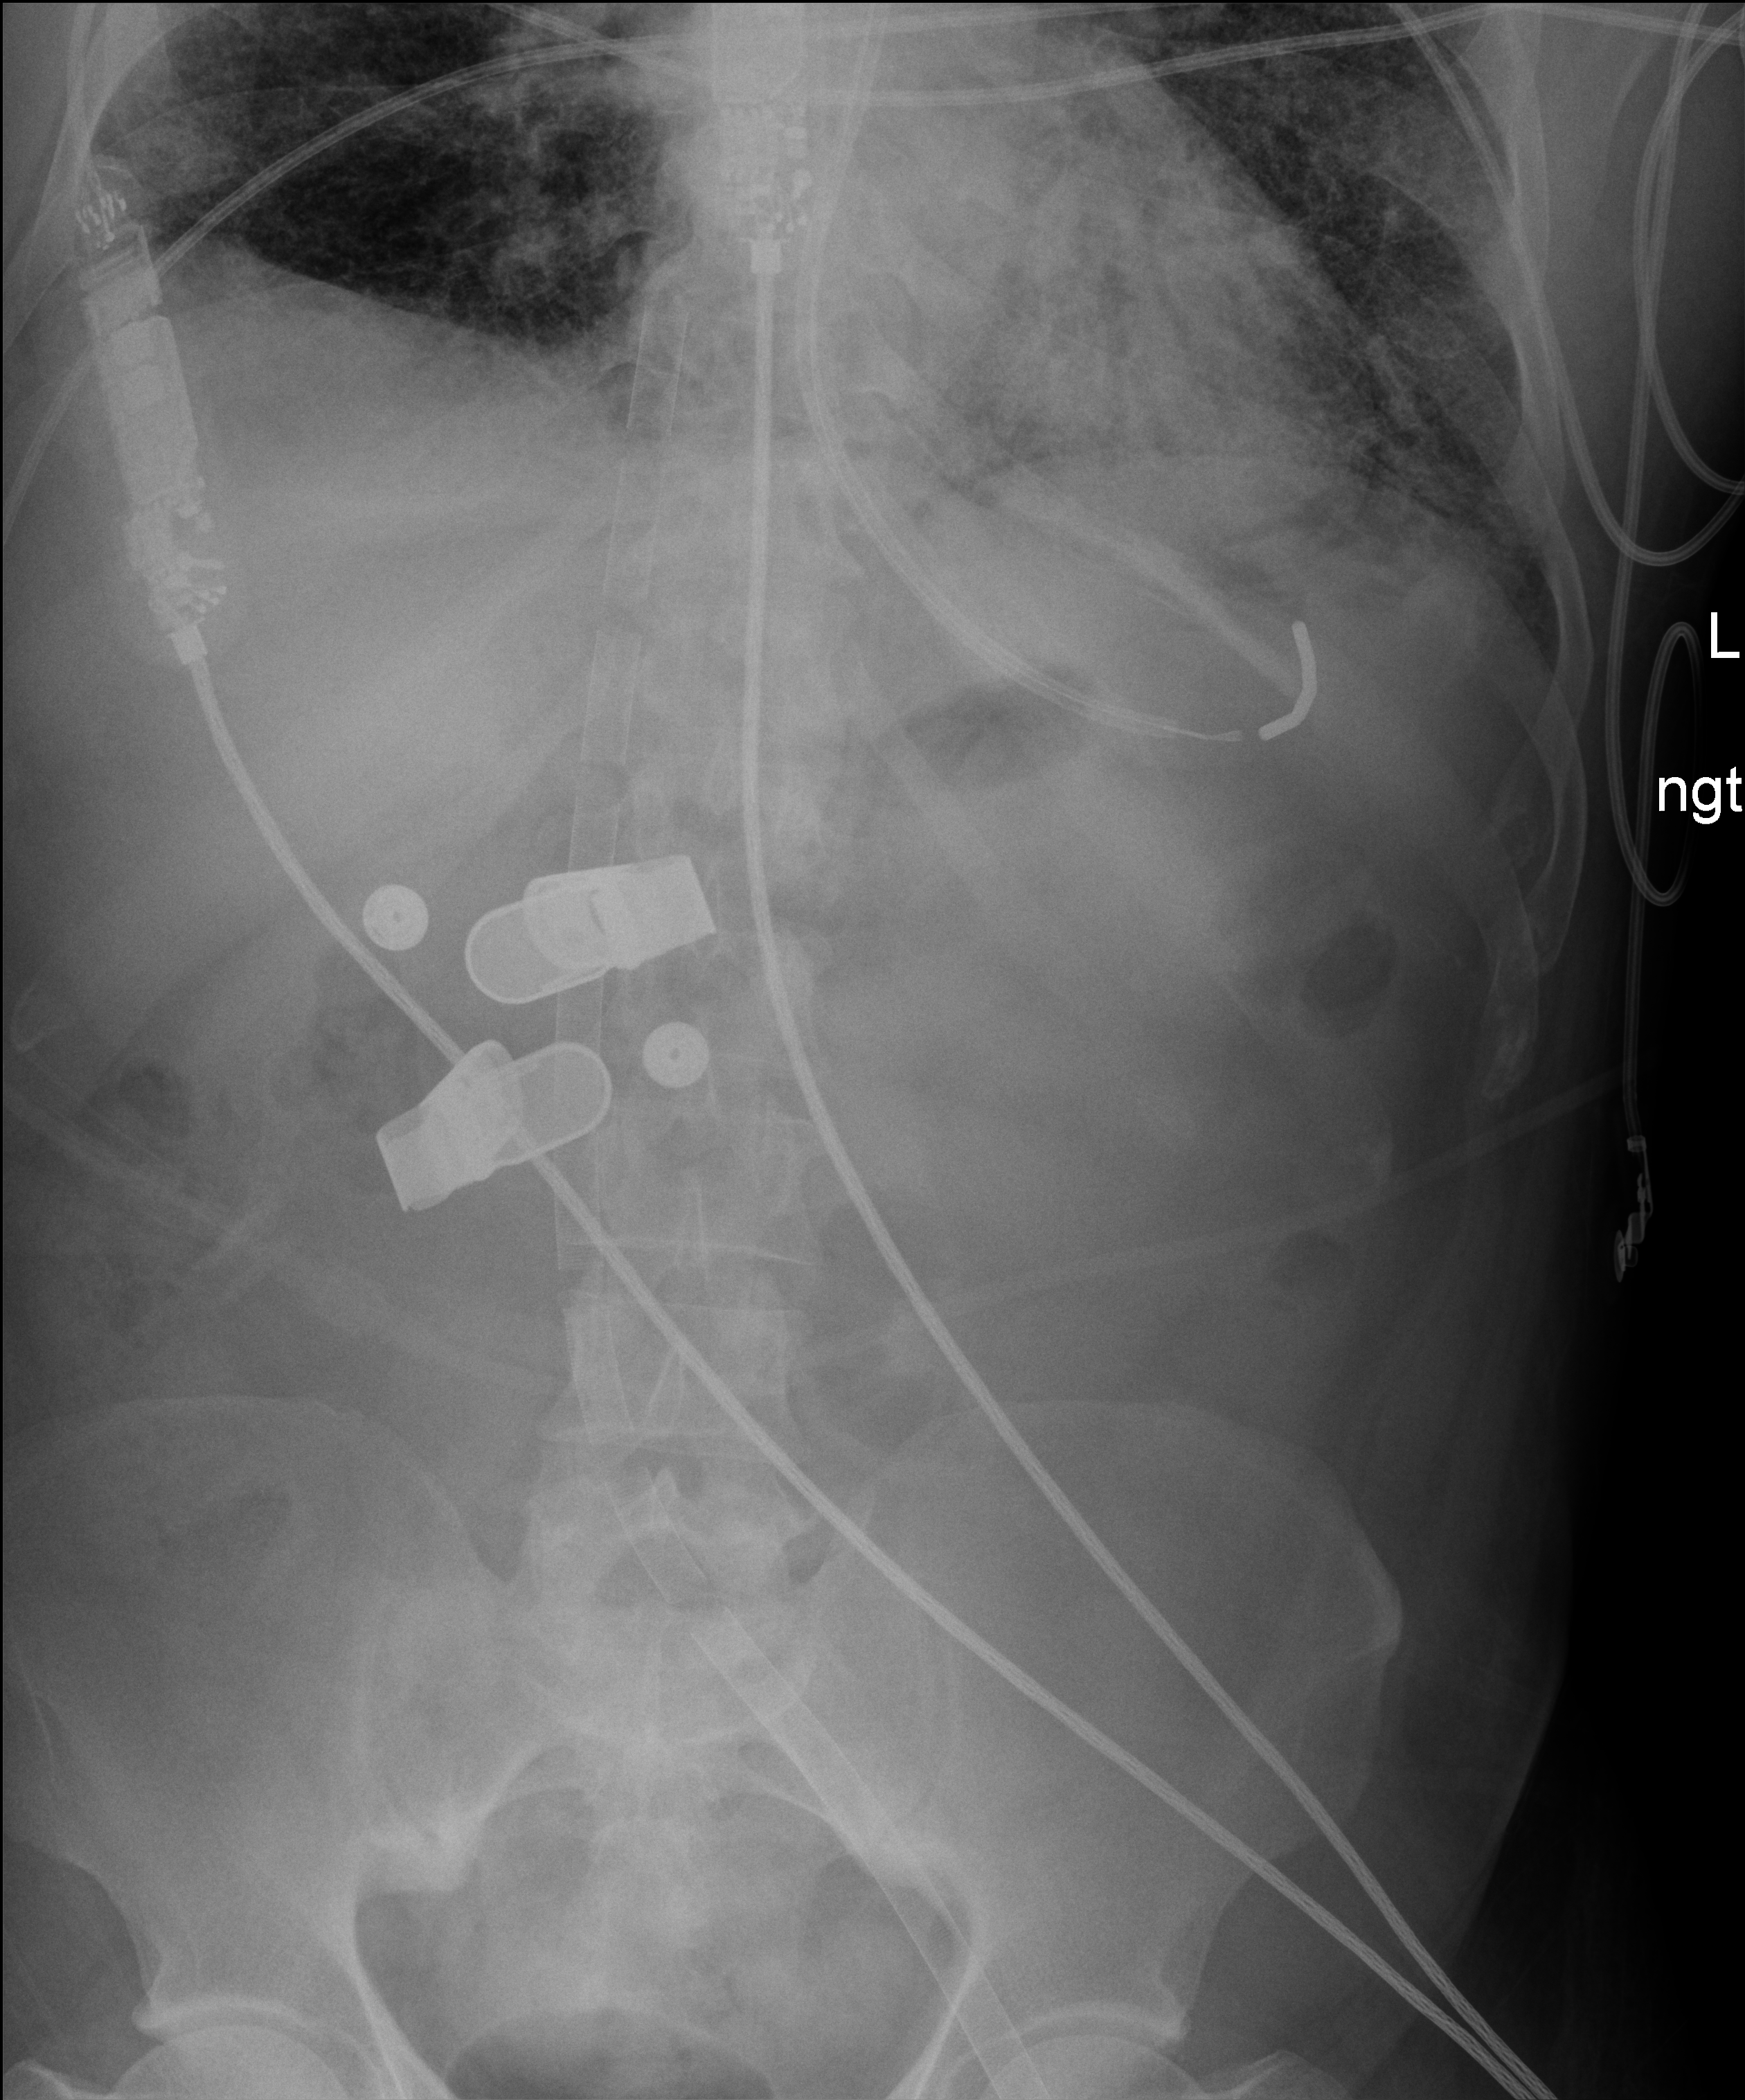
Portable chest radiograph, anteroposterior (AP) projection. Male patient hospitalised with COVID-19, age 18–59 years.
Hospital-stay facts (about this admission, not read from this image; timing relative to this image not recorded): smoking status (admission record): never.